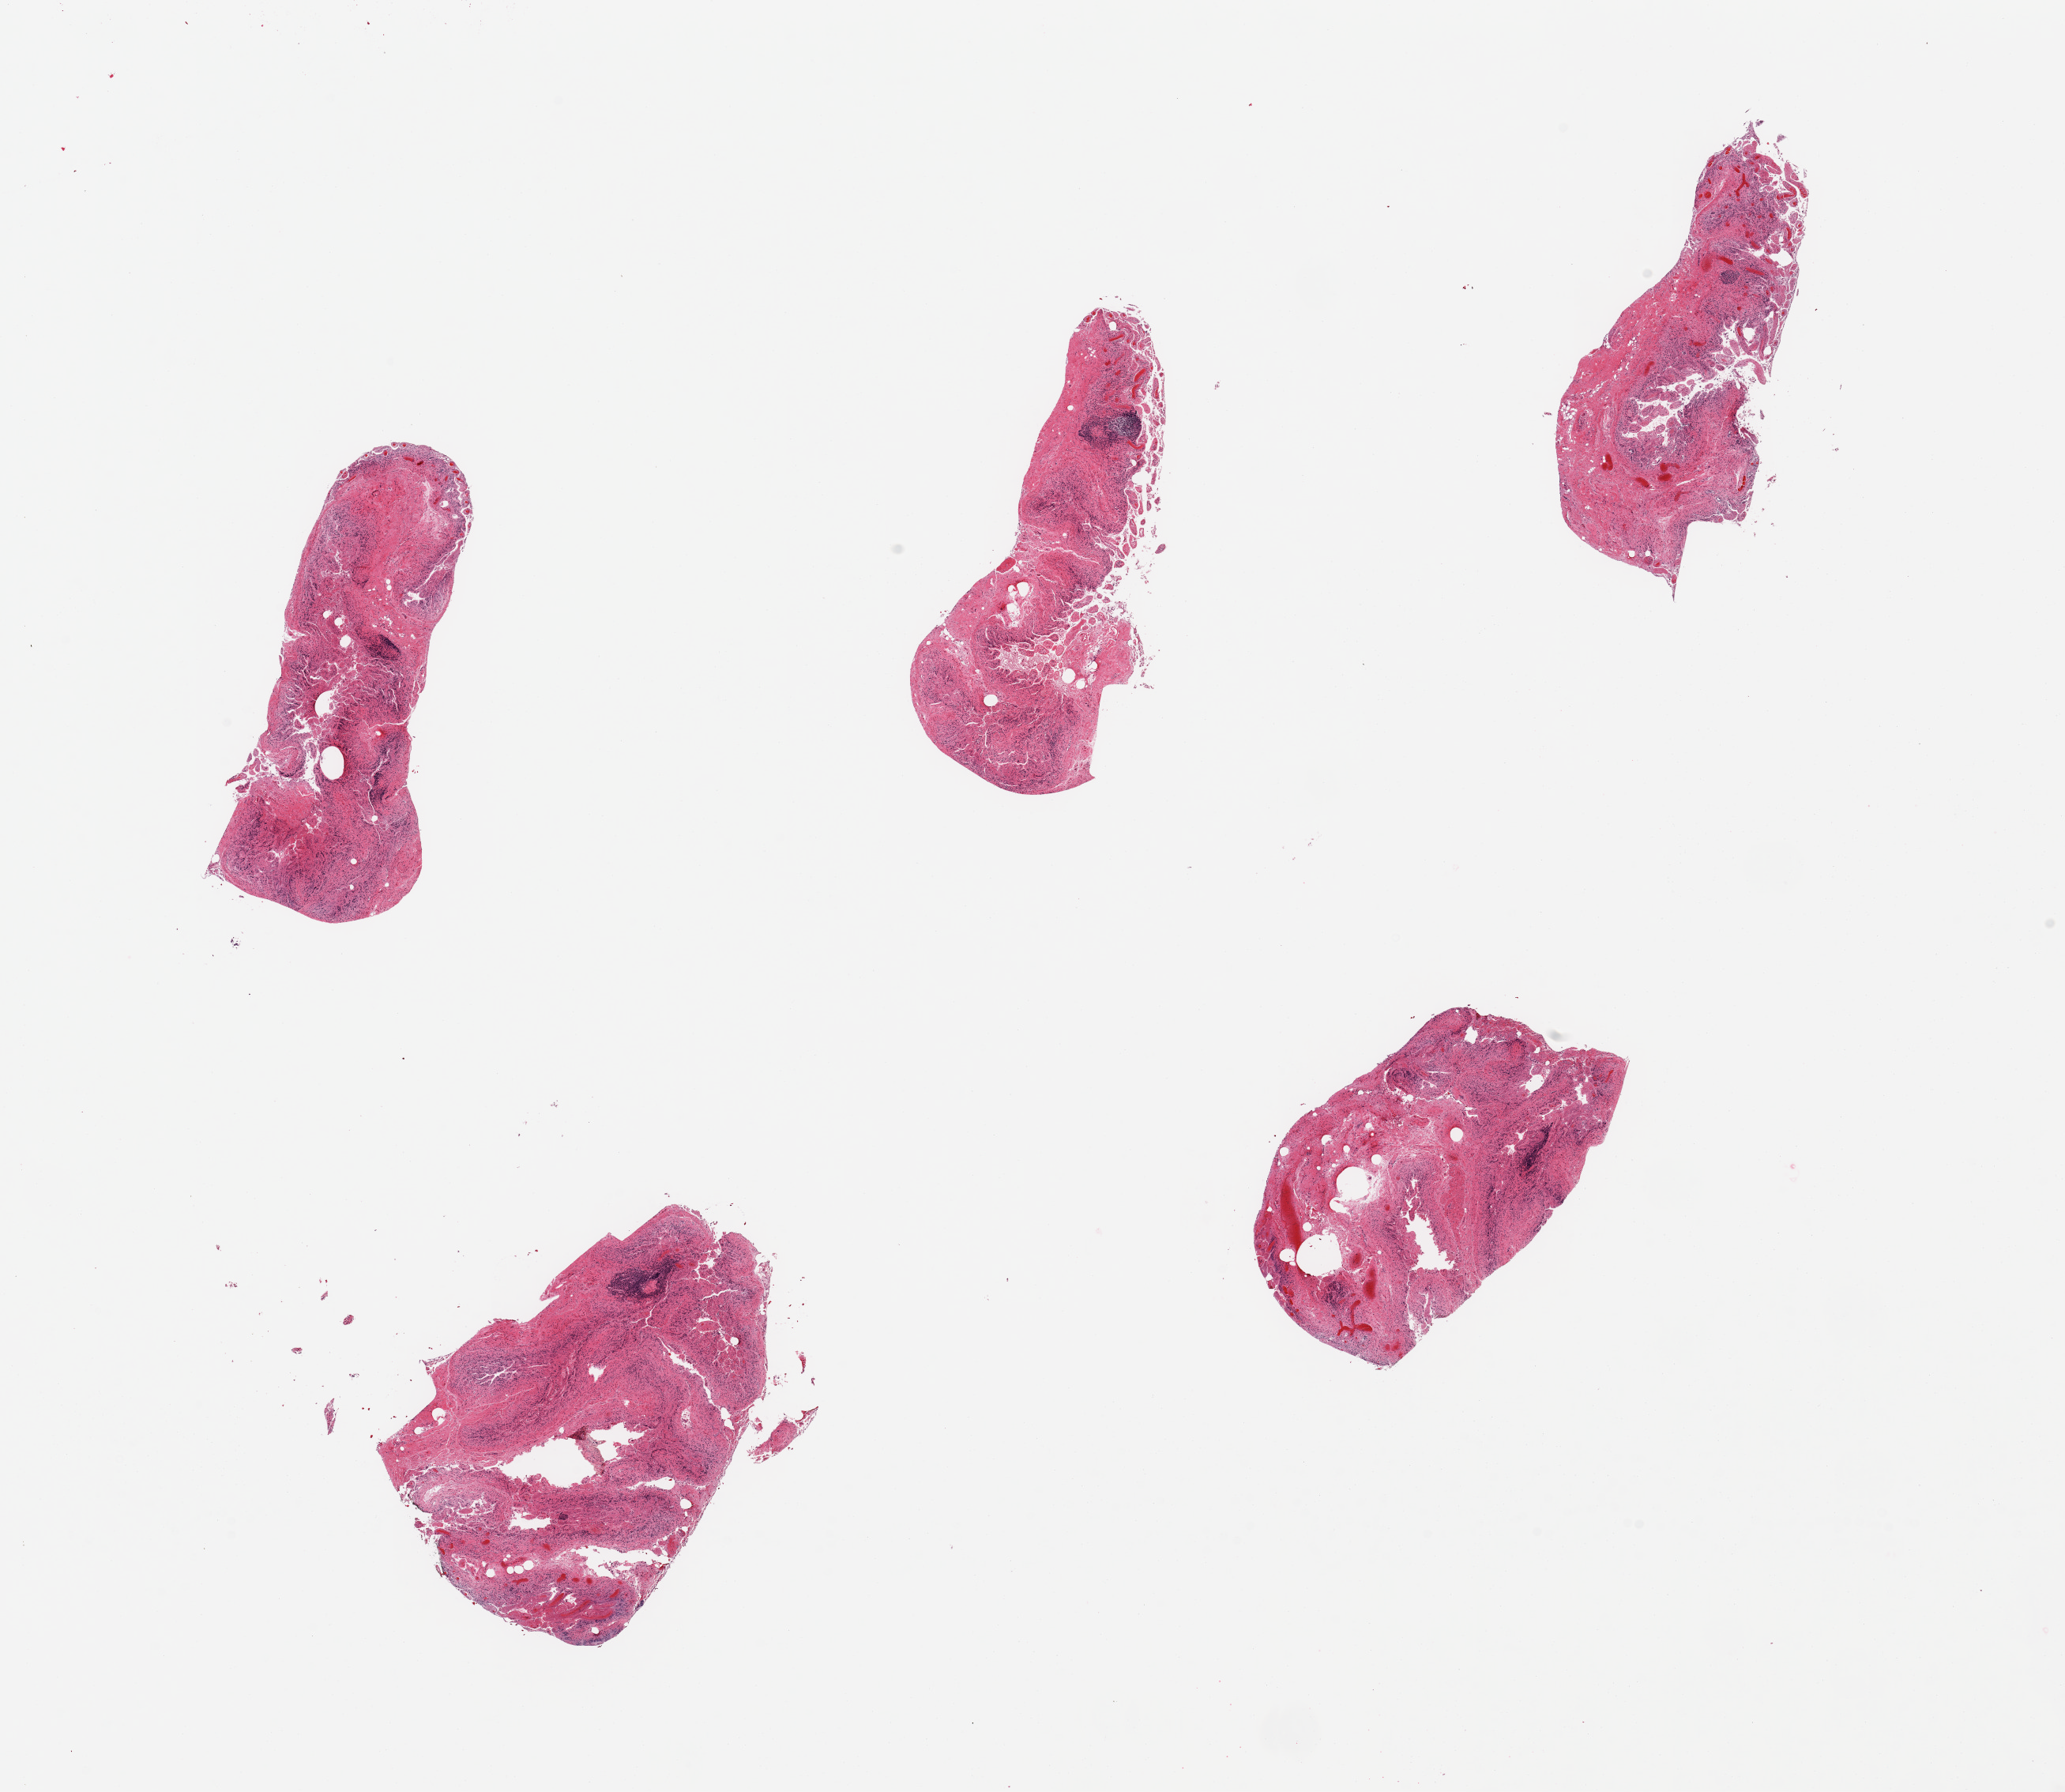
Haematoxylin and eosin whole-slide image, shown as a low-resolution overview of the whole scanned area (about 20.7 x 17.9 mm, acquisition: 20x scan); PAXgene-fixed paraffin-embedded (PFPE) section; sampled site (target tissue): ileum; donor tissue sample. Male donor.
Pathologist's review note for this sample: 5 pieces; totally autolyzed mucosa; too few lymphoid aggregates to warrant analysis.